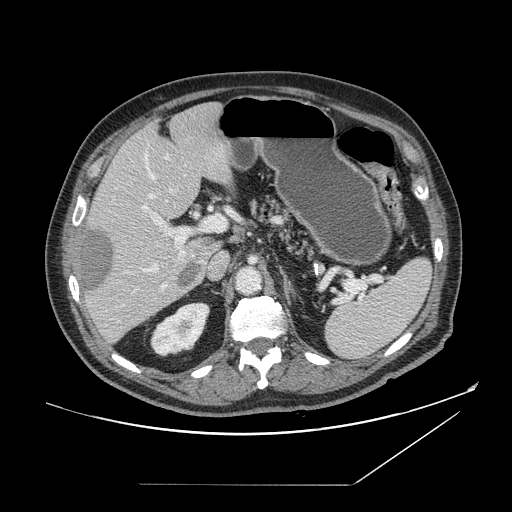
Contrast-enhanced abdominal CT, one axial slice. Slice 96 of 166 in the series (ordered by position). Intravenous contrast given. Soft-tissue window (W 400 / L 40 HU). 2.5 mm slice thickness. 512 × 512 image matrix, field of view 416 × 416 mm. Male patient, age 80 years. From the clinical record (not read from this slice): diagnosis: colorectal cancer liver metastases, imaged before liver resection; multiple liver metastases: no; largest metastasis: 2.2 cm; disease in both lobes: no.
Outlined on this slice (expert manual segmentation):
- hepatic veins: bounding box [x1, y1, x2, y2] px = [142, 153, 173, 272]
- liver: [77, 102, 235, 343]
- planned liver remnant (the part of the liver to remain after resection): [93, 102, 235, 255]
- portal vein (with intrahepatic branches): [142, 206, 227, 290]
- liver metastasis: [82, 229, 200, 299]